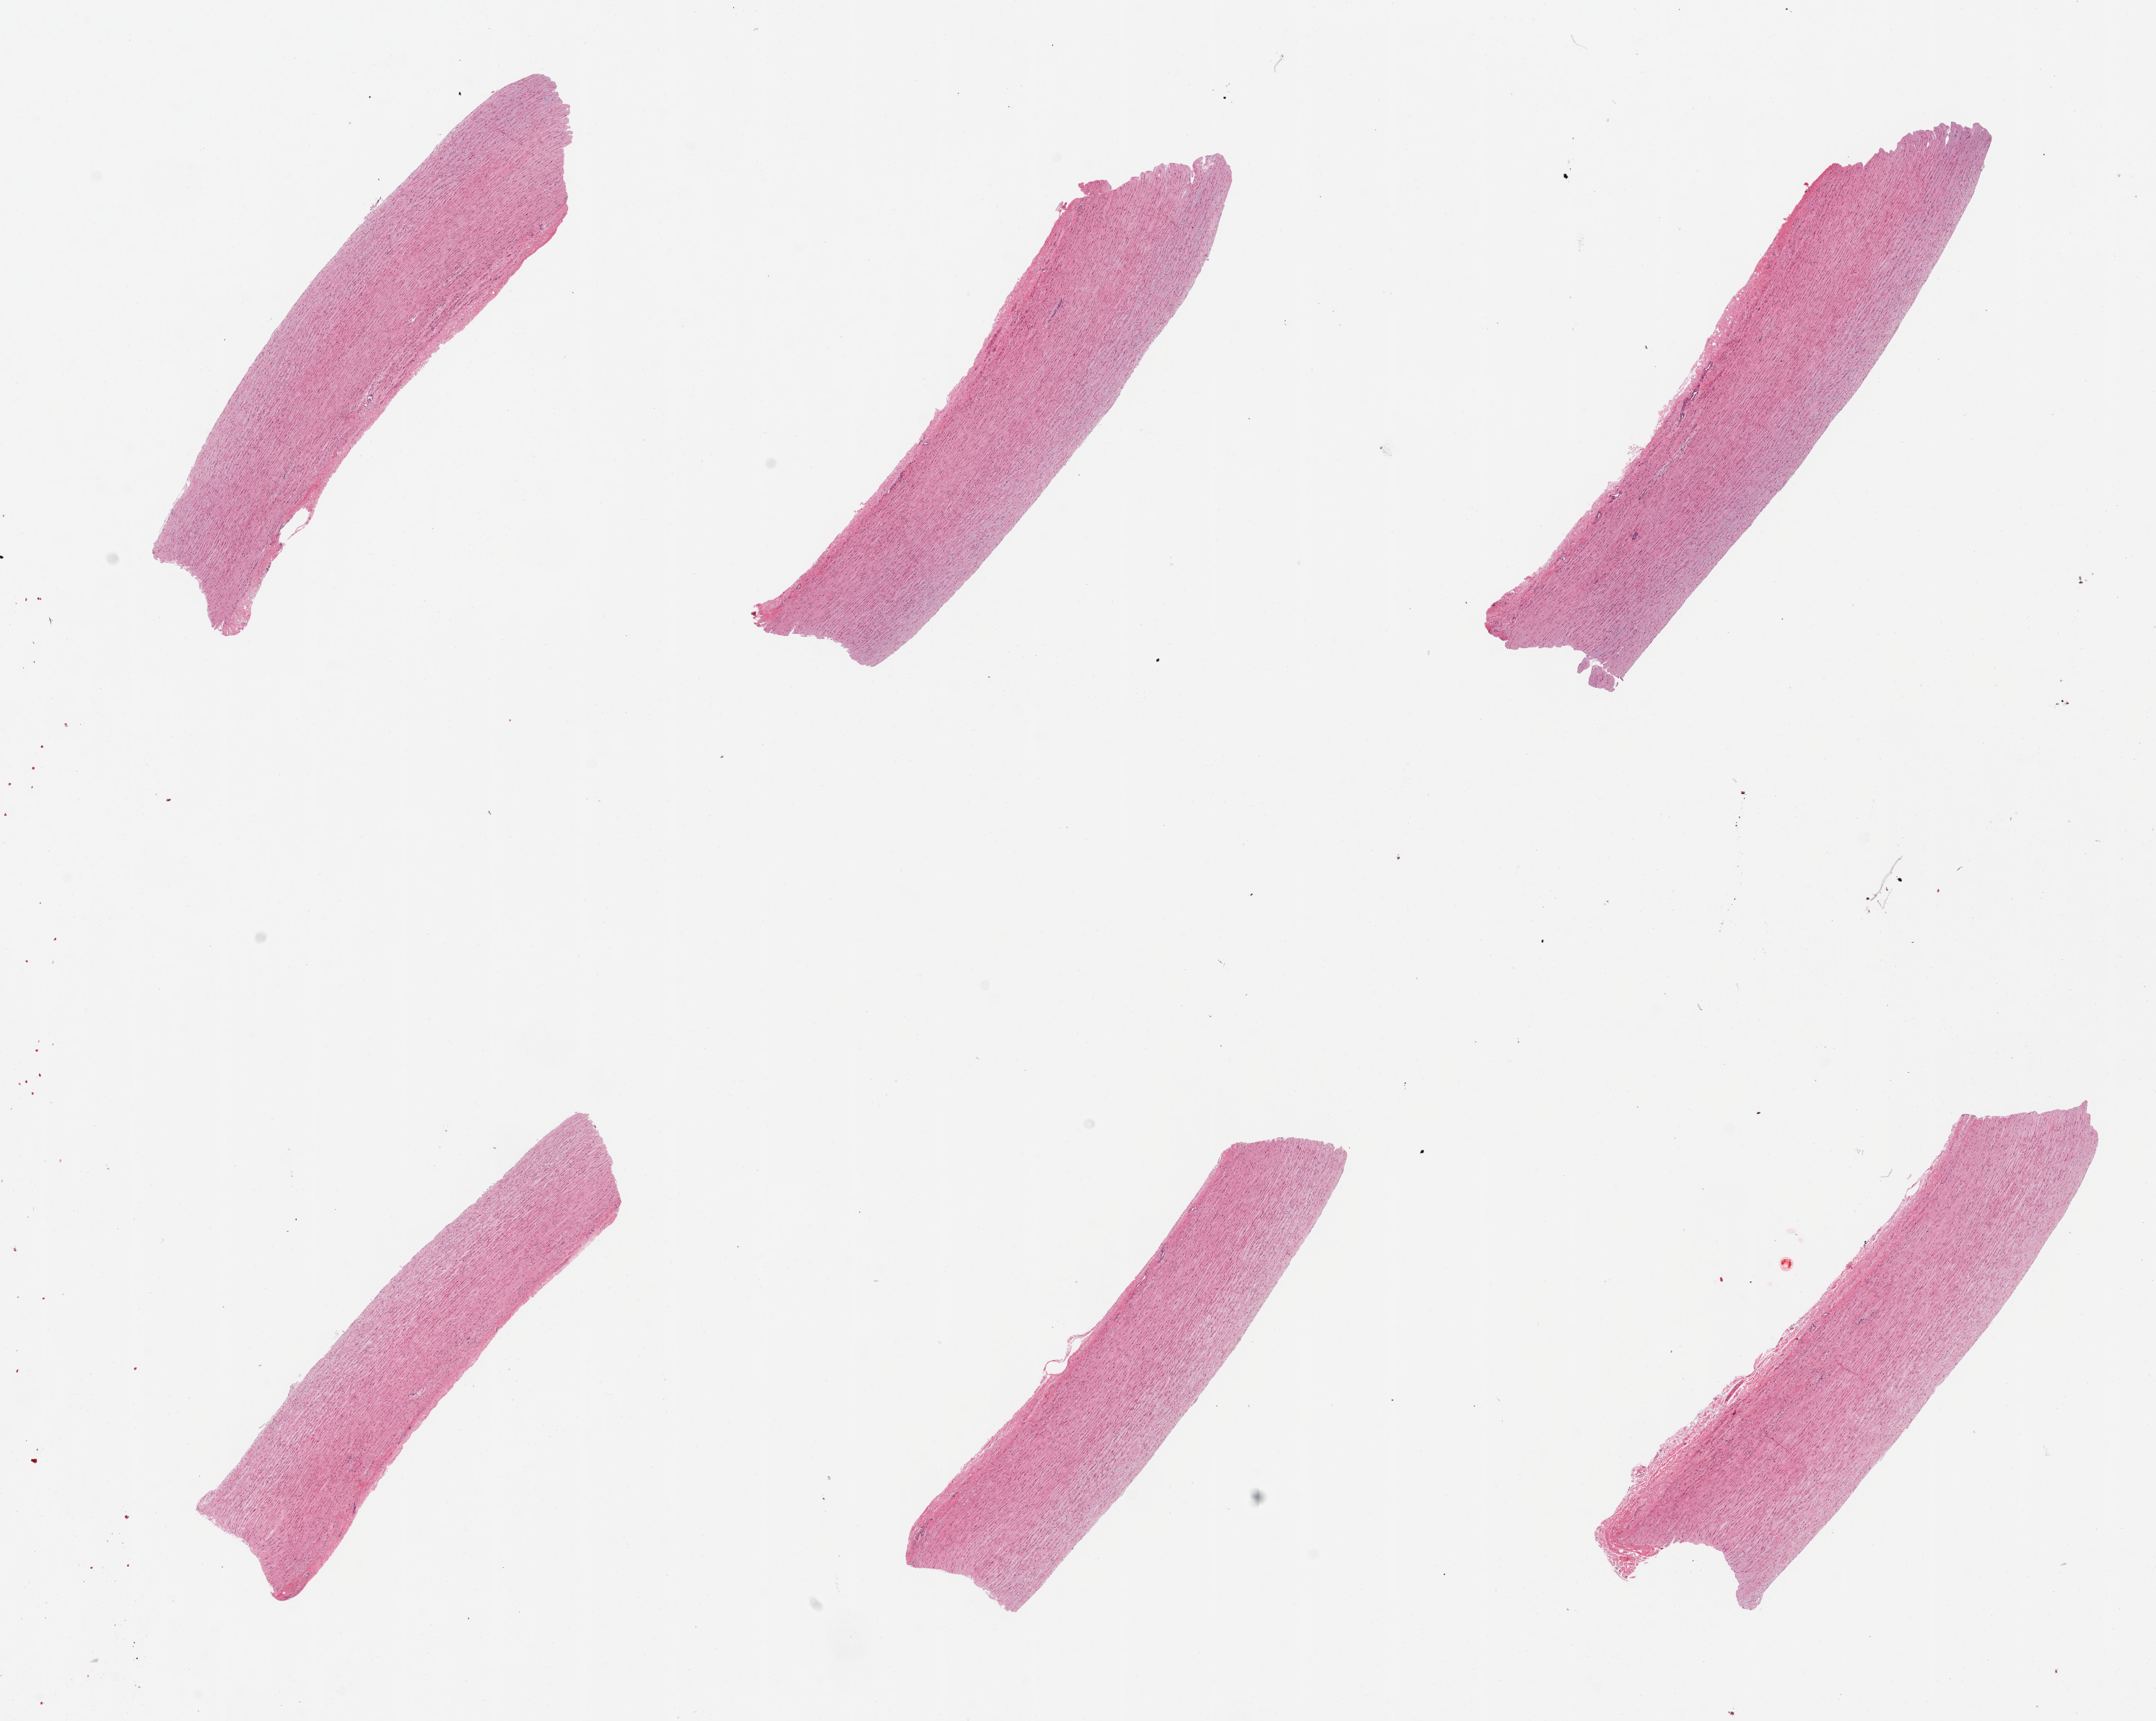
Whole-slide image, haematoxylin and eosin stain — low-resolution overview of the scanned area, about 23.6 x 18.9 mm (from a 20x scan), PAXgene-fixed paraffin-embedded (PFPE) section, section of aorta (target tissue), tissue donor sample. Donor: female.
Reviewer comment on this tissue sample: 6 pieces.